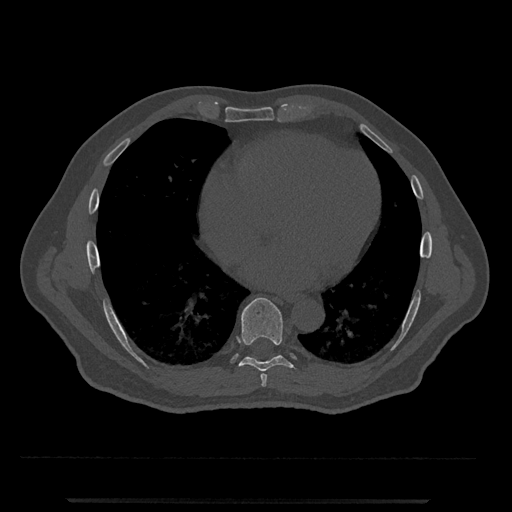
CT including the spine, one axial slice; slice 624 of 797 in the series (ordered by position); bone window (W 1800 / L 400 HU); 0.5 mm slice thickness; 512 × 512 image matrix, field of view 419 × 419 mm. Patient: male, 63 years. Case-level facts recorded for this patient, not image findings: primary cancer: prostate.
Annotated regions visible in this slice (semi-automatic segmentation, software-assisted and operator-edited):
- T7 vertebra: bounding box (x1, y1, x2, y2) in pixels: (260, 374, 267, 387)
- T8 vertebra: (233, 298, 294, 372)